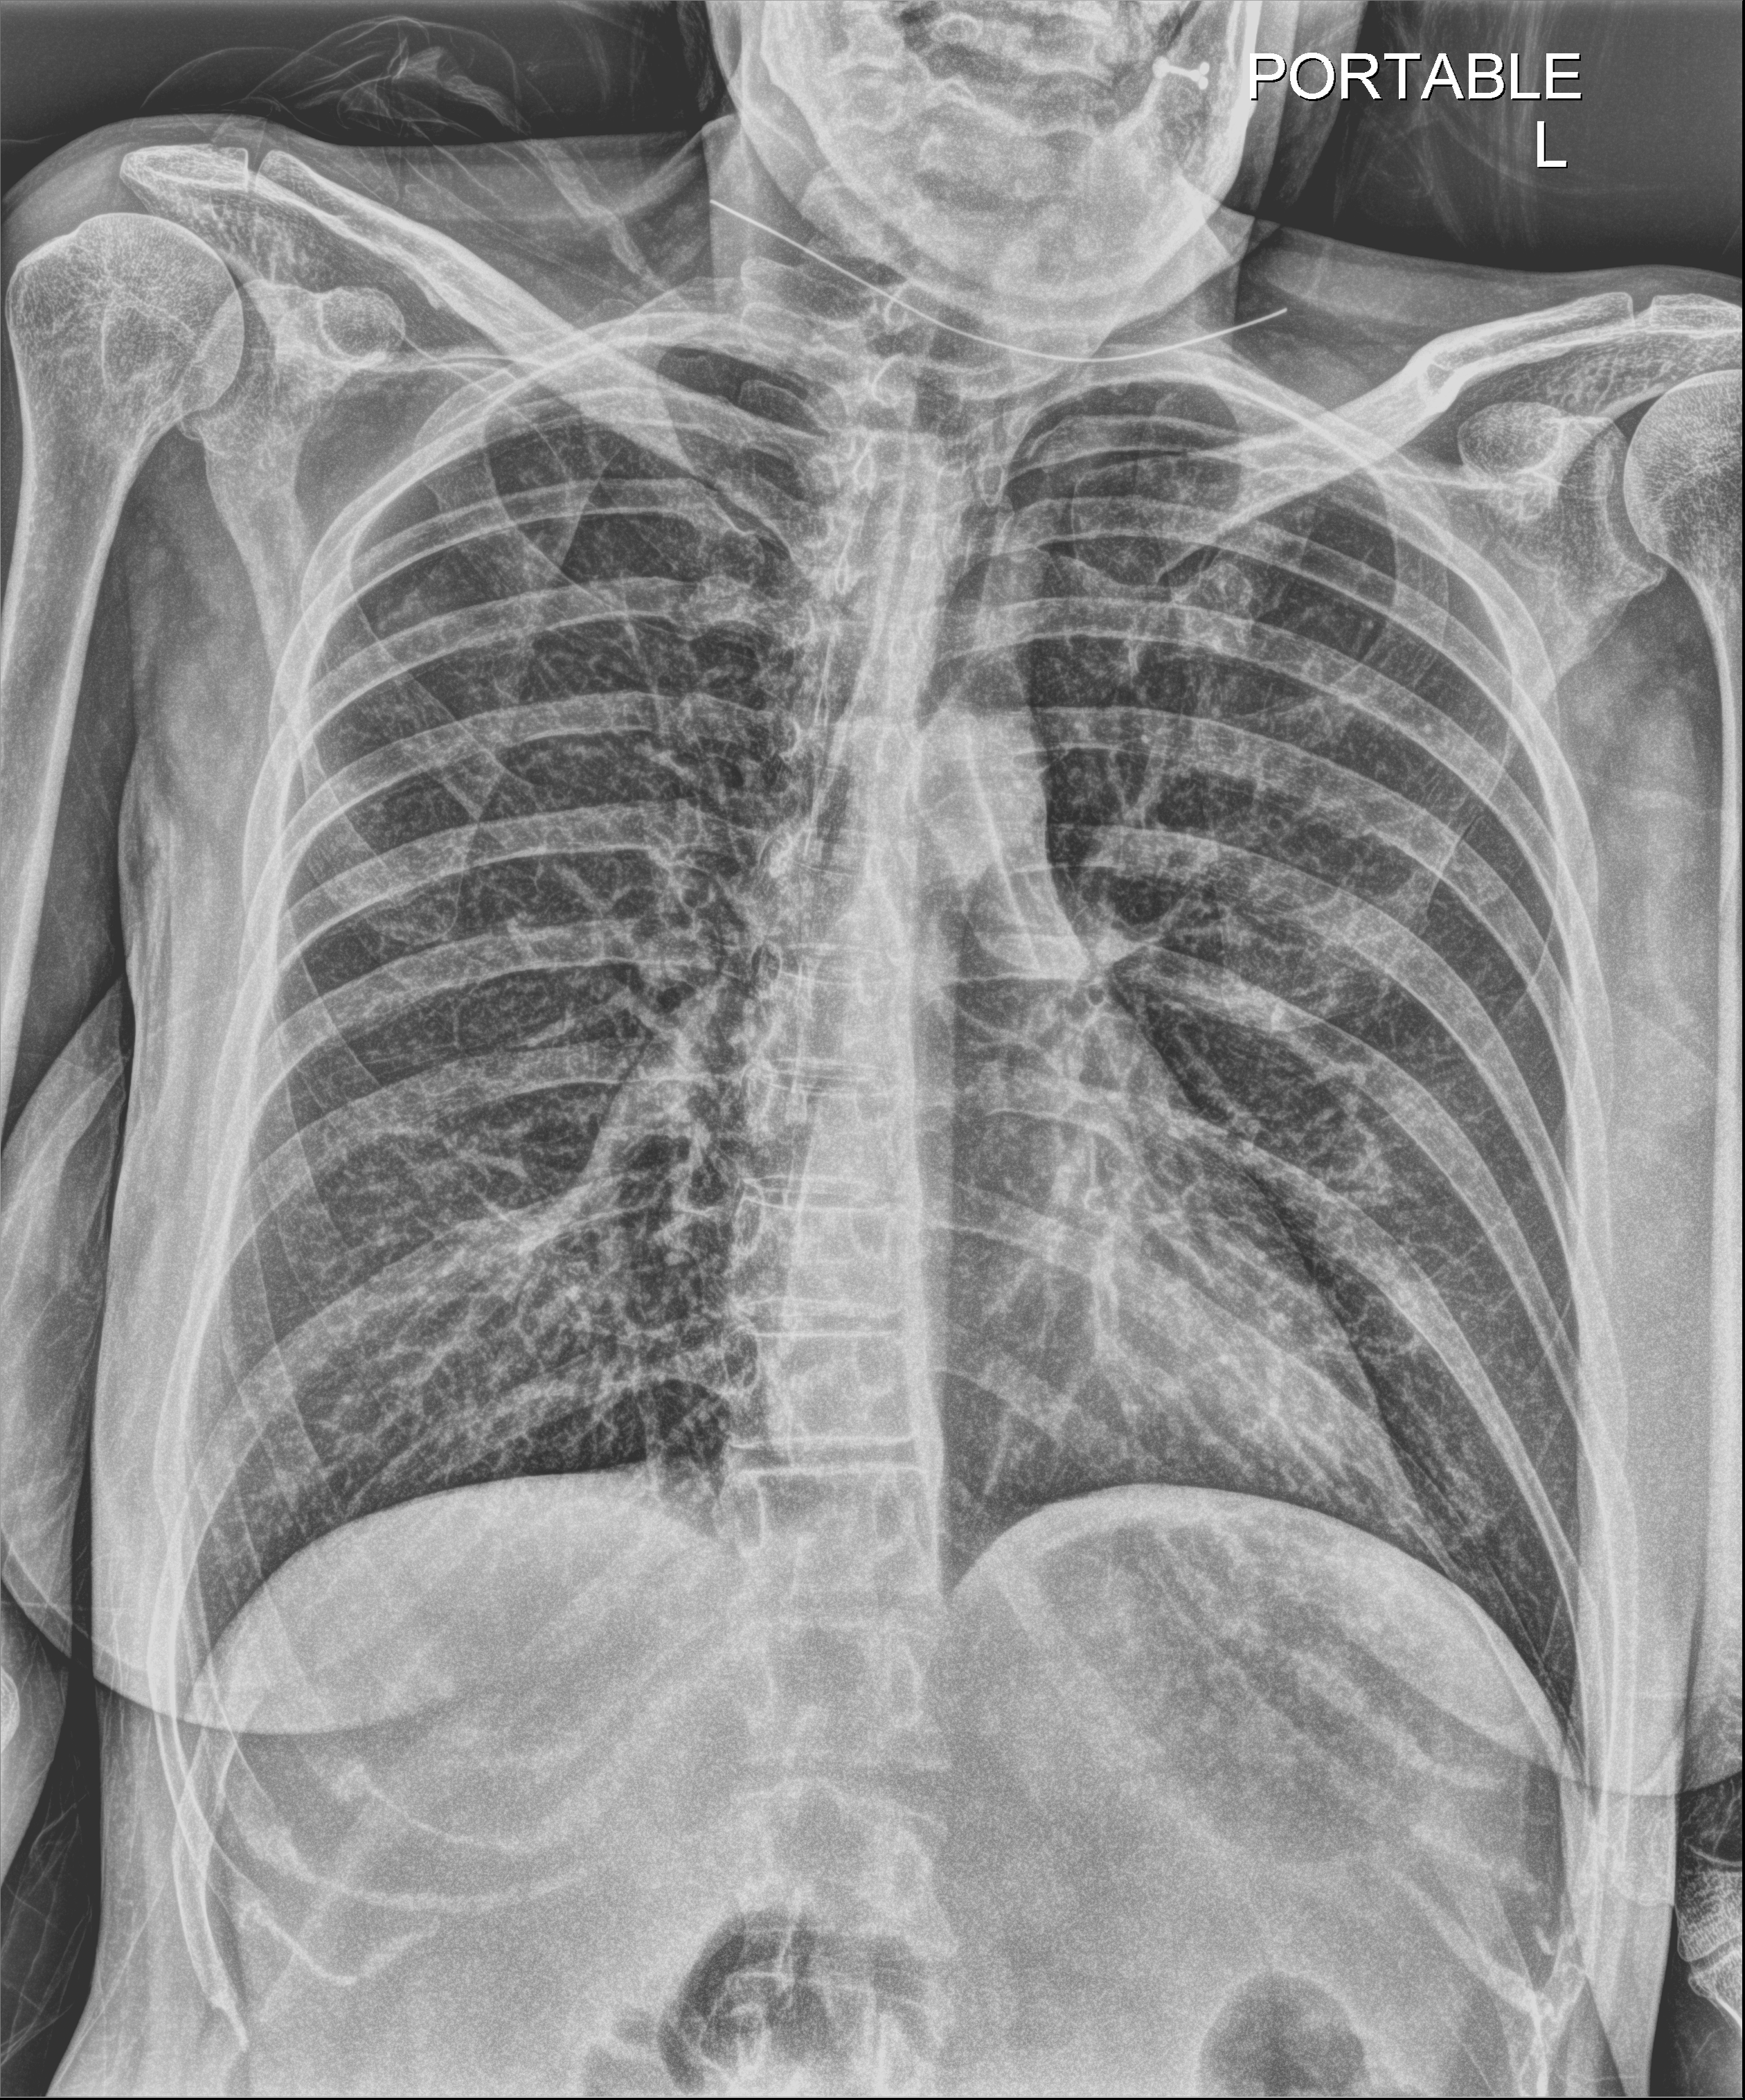
Chest radiograph (digital radiography); anteroposterior (AP) projection. Patient hospitalised with COVID-19; female, aged 18–59 years.
From the hospital-stay record, not from the radiograph (when in the stay this image was taken is not recorded): length of hospital stay: 7 days.